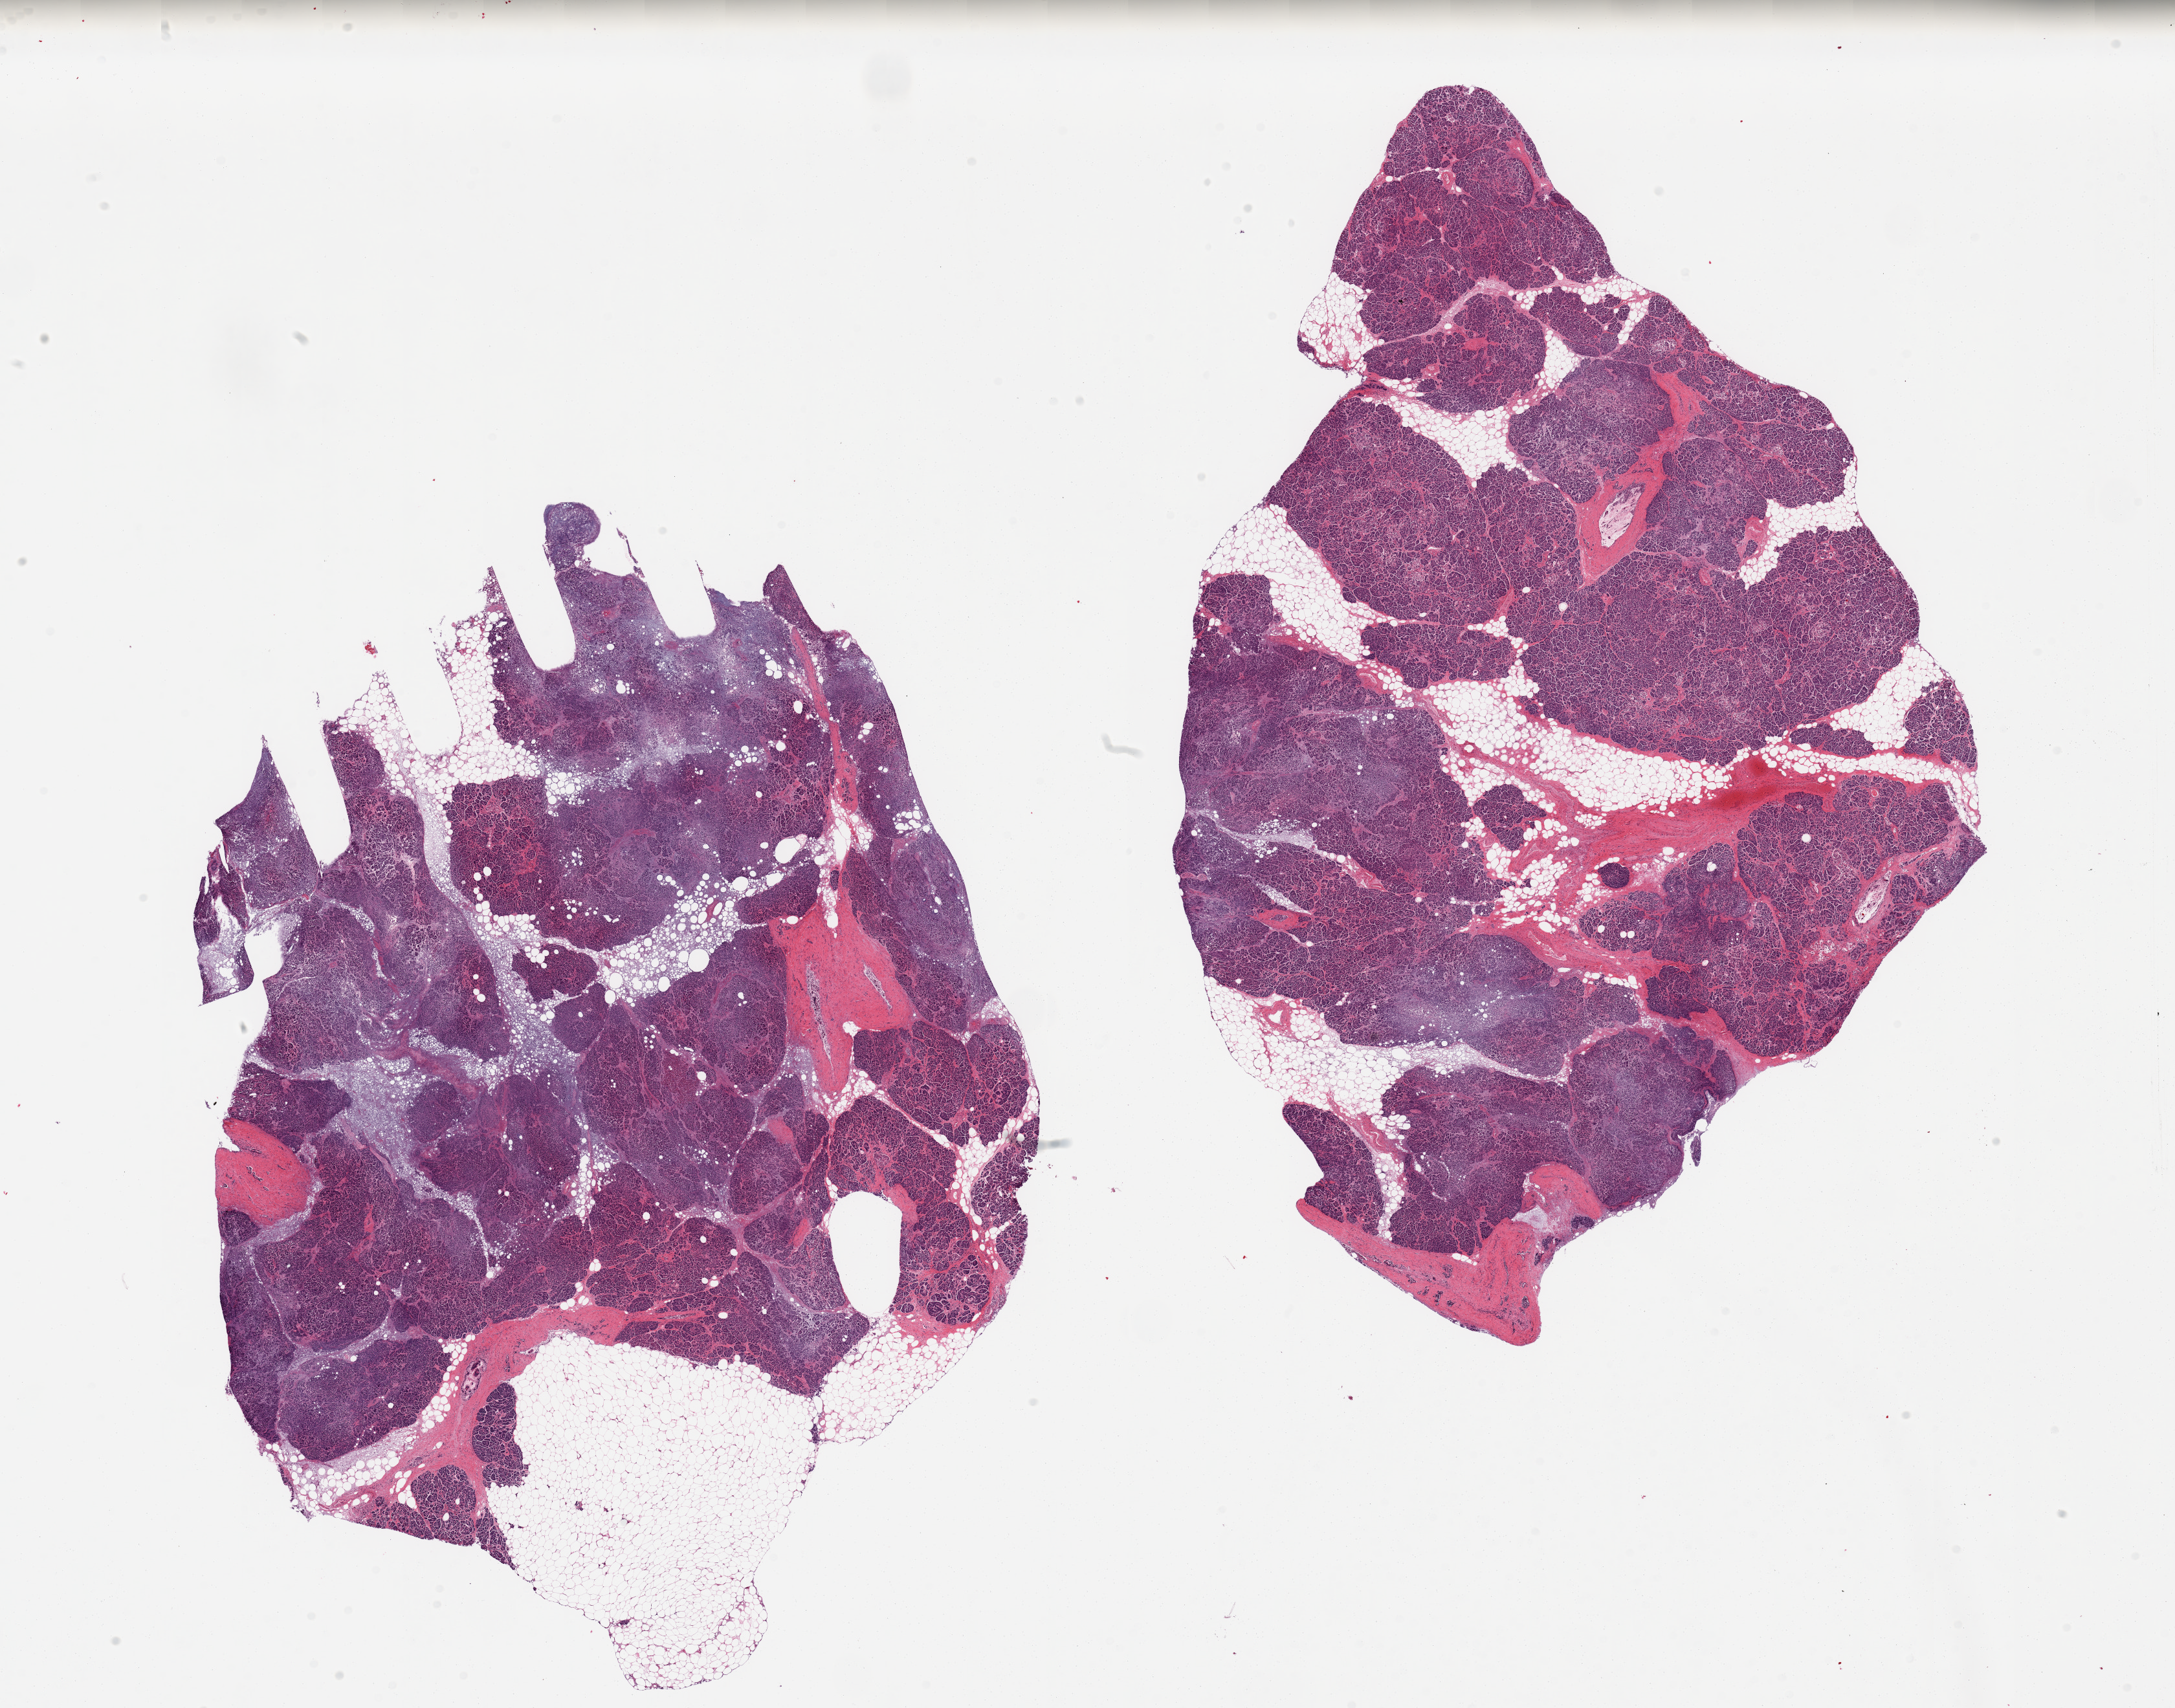
H&E whole-slide image — shown as a low-resolution overview of the whole scanned area (about 26.6 x 20.9 mm); PAXgene-fixed paraffin-embedded (PFPE) section; sampled site (target tissue): pancreas; tissue donor sample. Donor sex: male.
• reviewer comment on this tissue sample: 2 pieces, moderate saponification, Islets not well seen, attached nubbins of fat, ~4mm